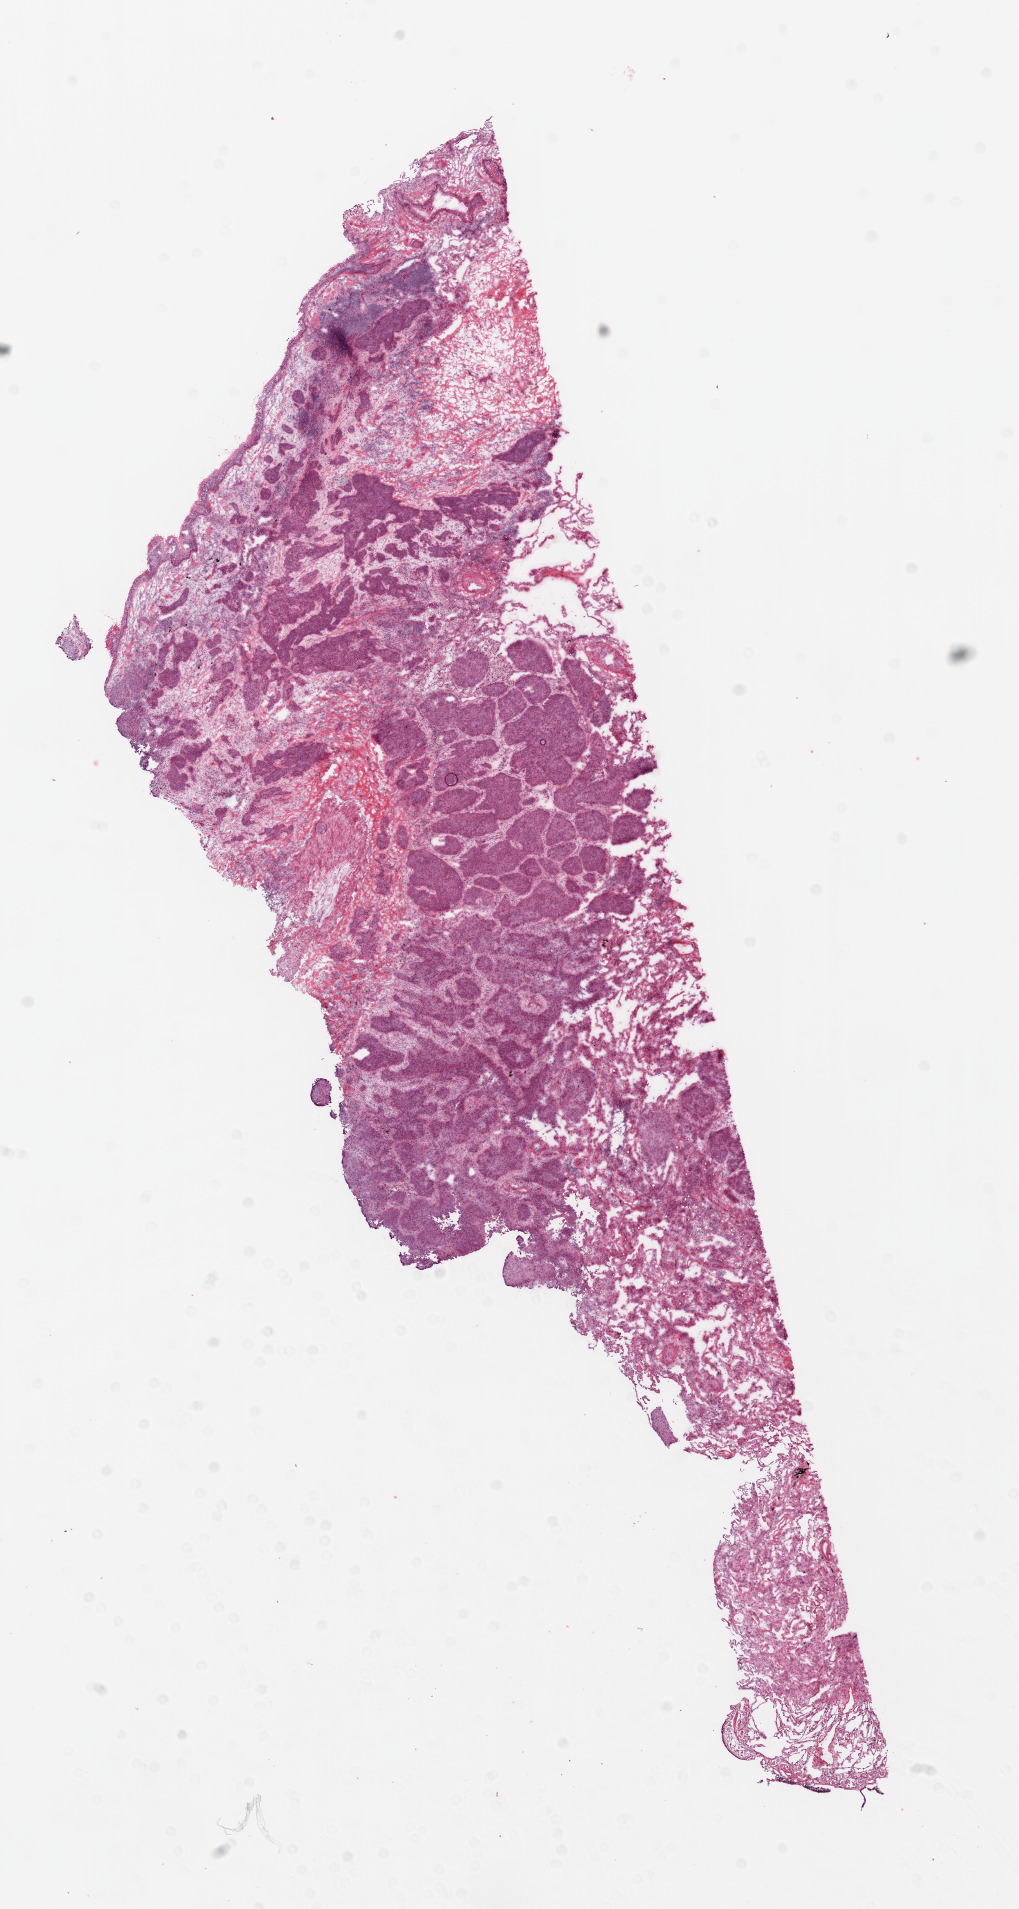
Whole-slide histology image, H&E-stained, shown as a low-resolution overview of the whole scanned area (about 8.2 x 15.4 mm, slide scanned at 20x), frozen section from the top of the tissue portion, sample: primary tumour, lung. Male patient; age at initial diagnosis 69 years. Slide review estimates, as recorded: tumour nuclei 60%, necrosis 0%.
Pathologic diagnosis: Squamous cell carcinoma, NOS. Laterality: right. AJCC pathologic stage: IA.